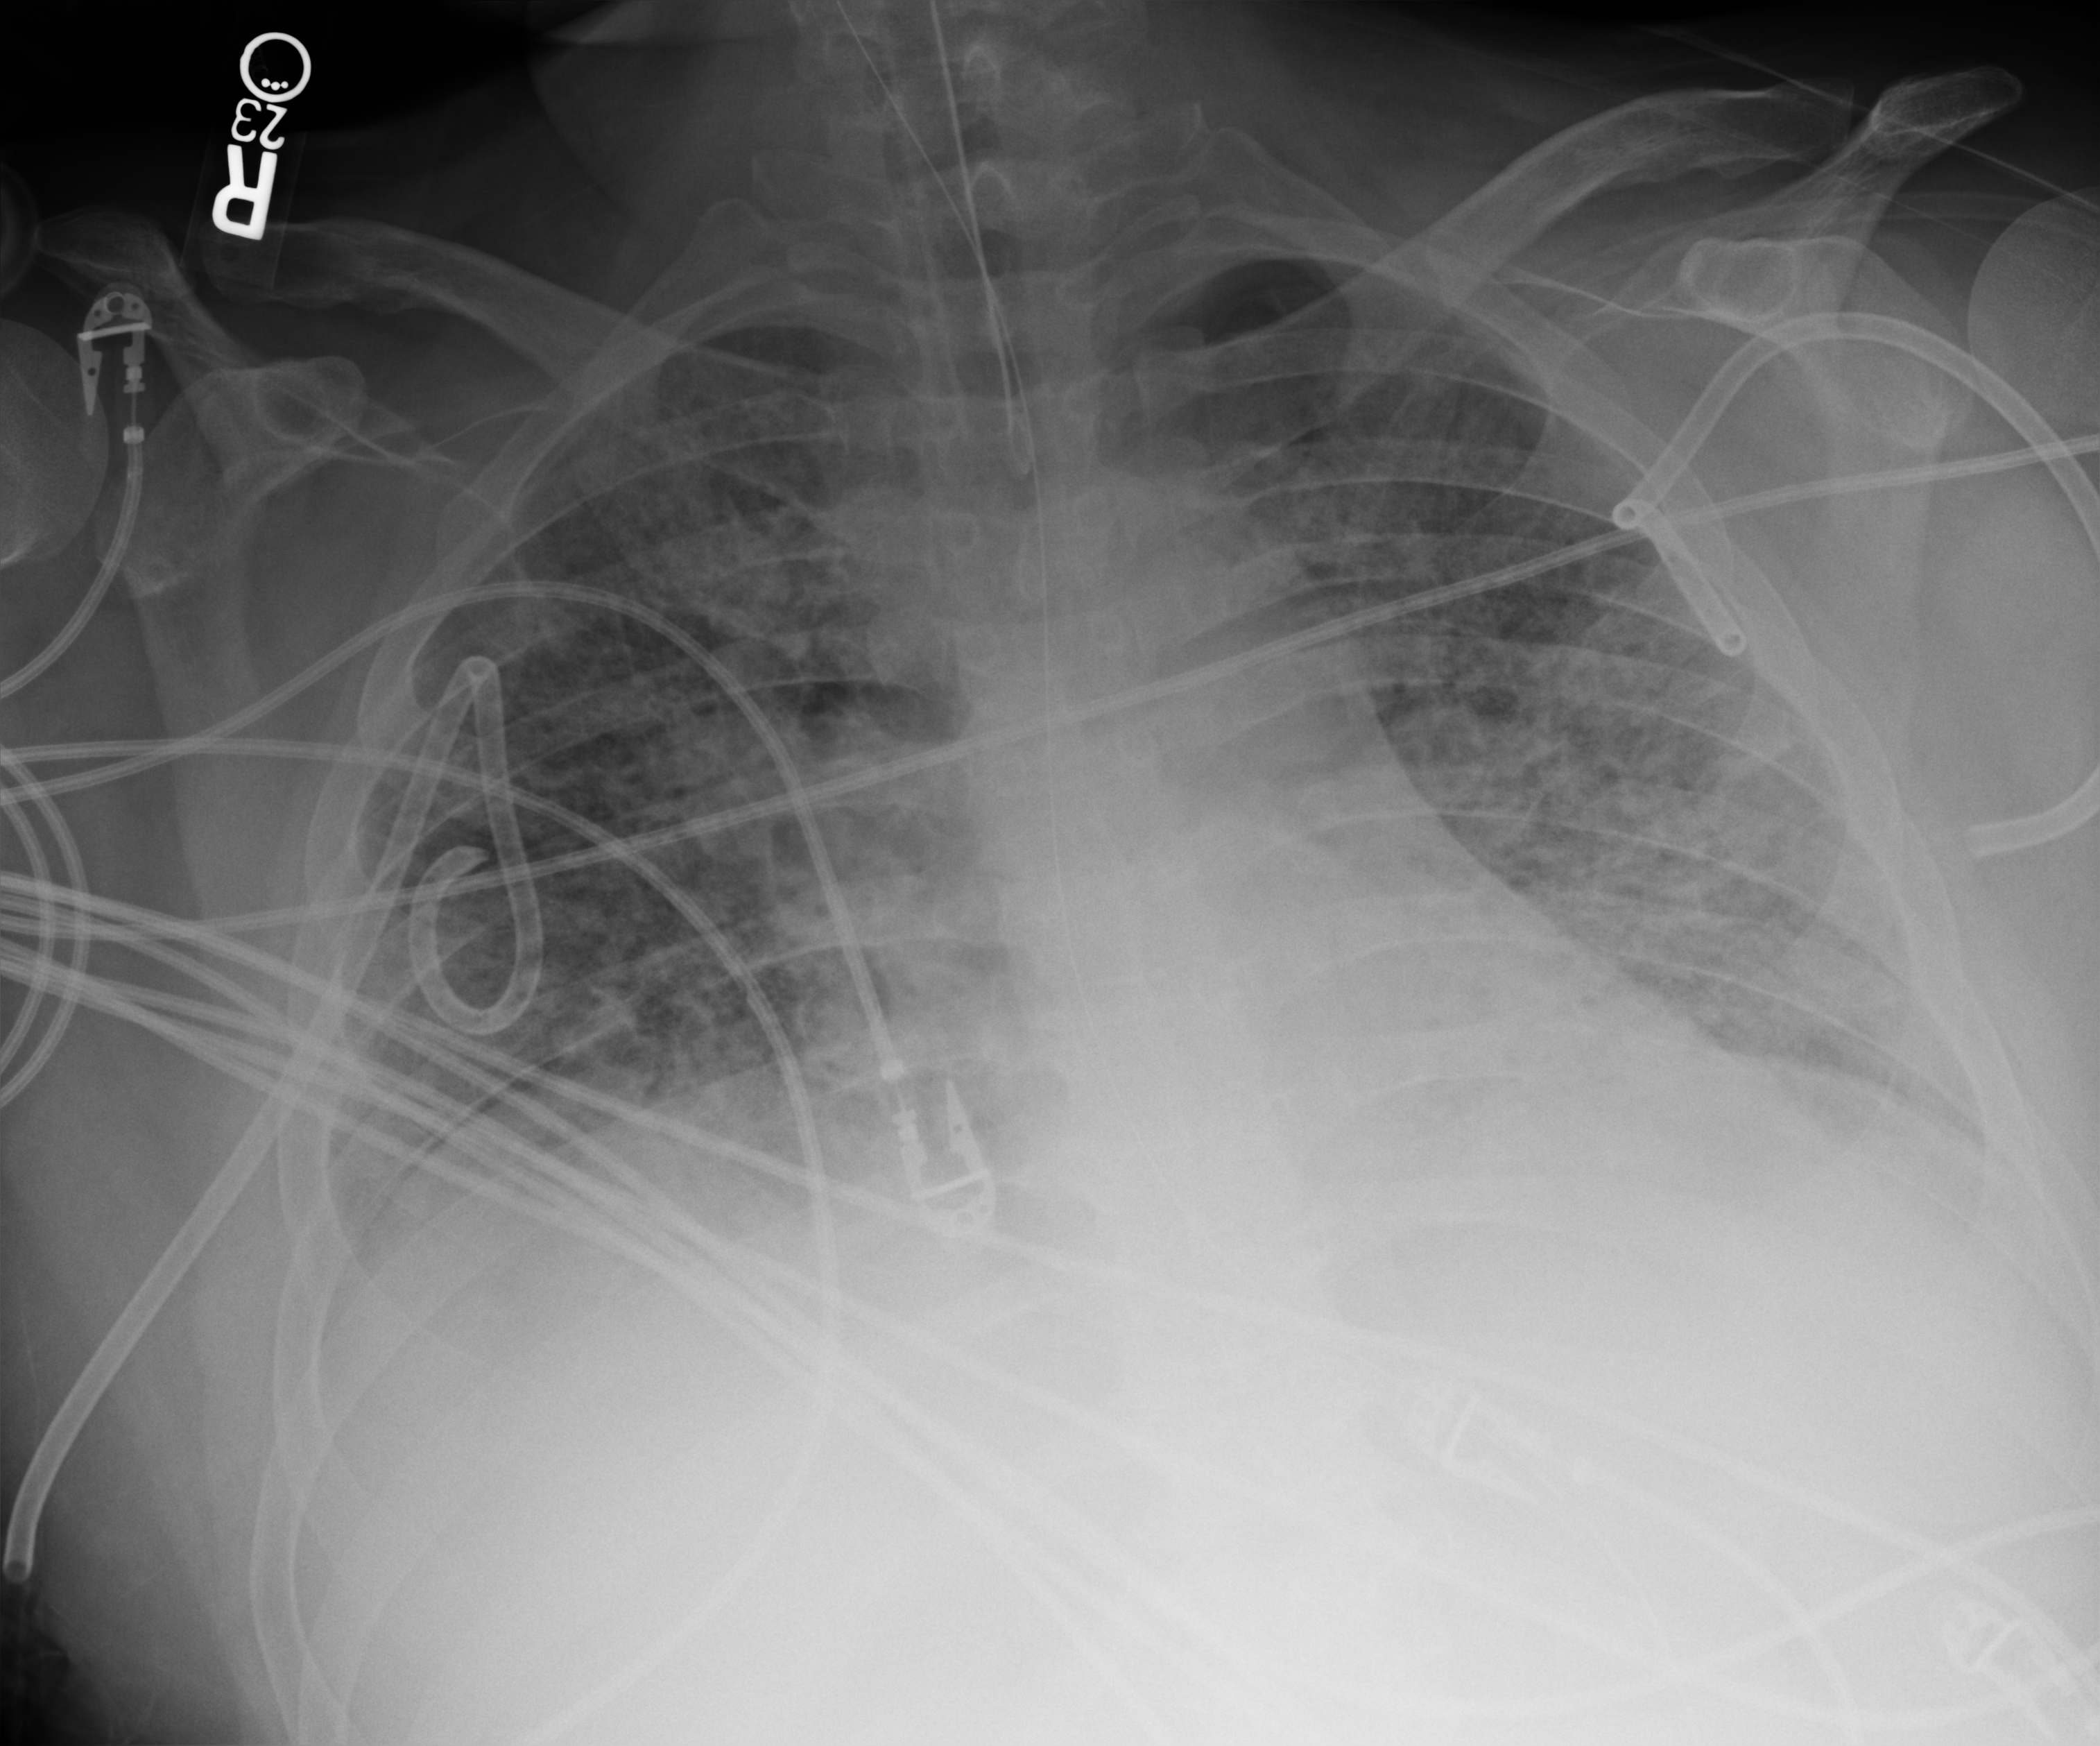
Bedside chest radiograph (computed radiography); anteroposterior (AP) projection. Patient hospitalised with COVID-19, aged 18–59 years.
Hospital-stay facts (about this admission, not read from this image; timing relative to this image not recorded): admitted to intensive care during this hospital stay: yes; mechanically ventilated during this hospital stay: yes.